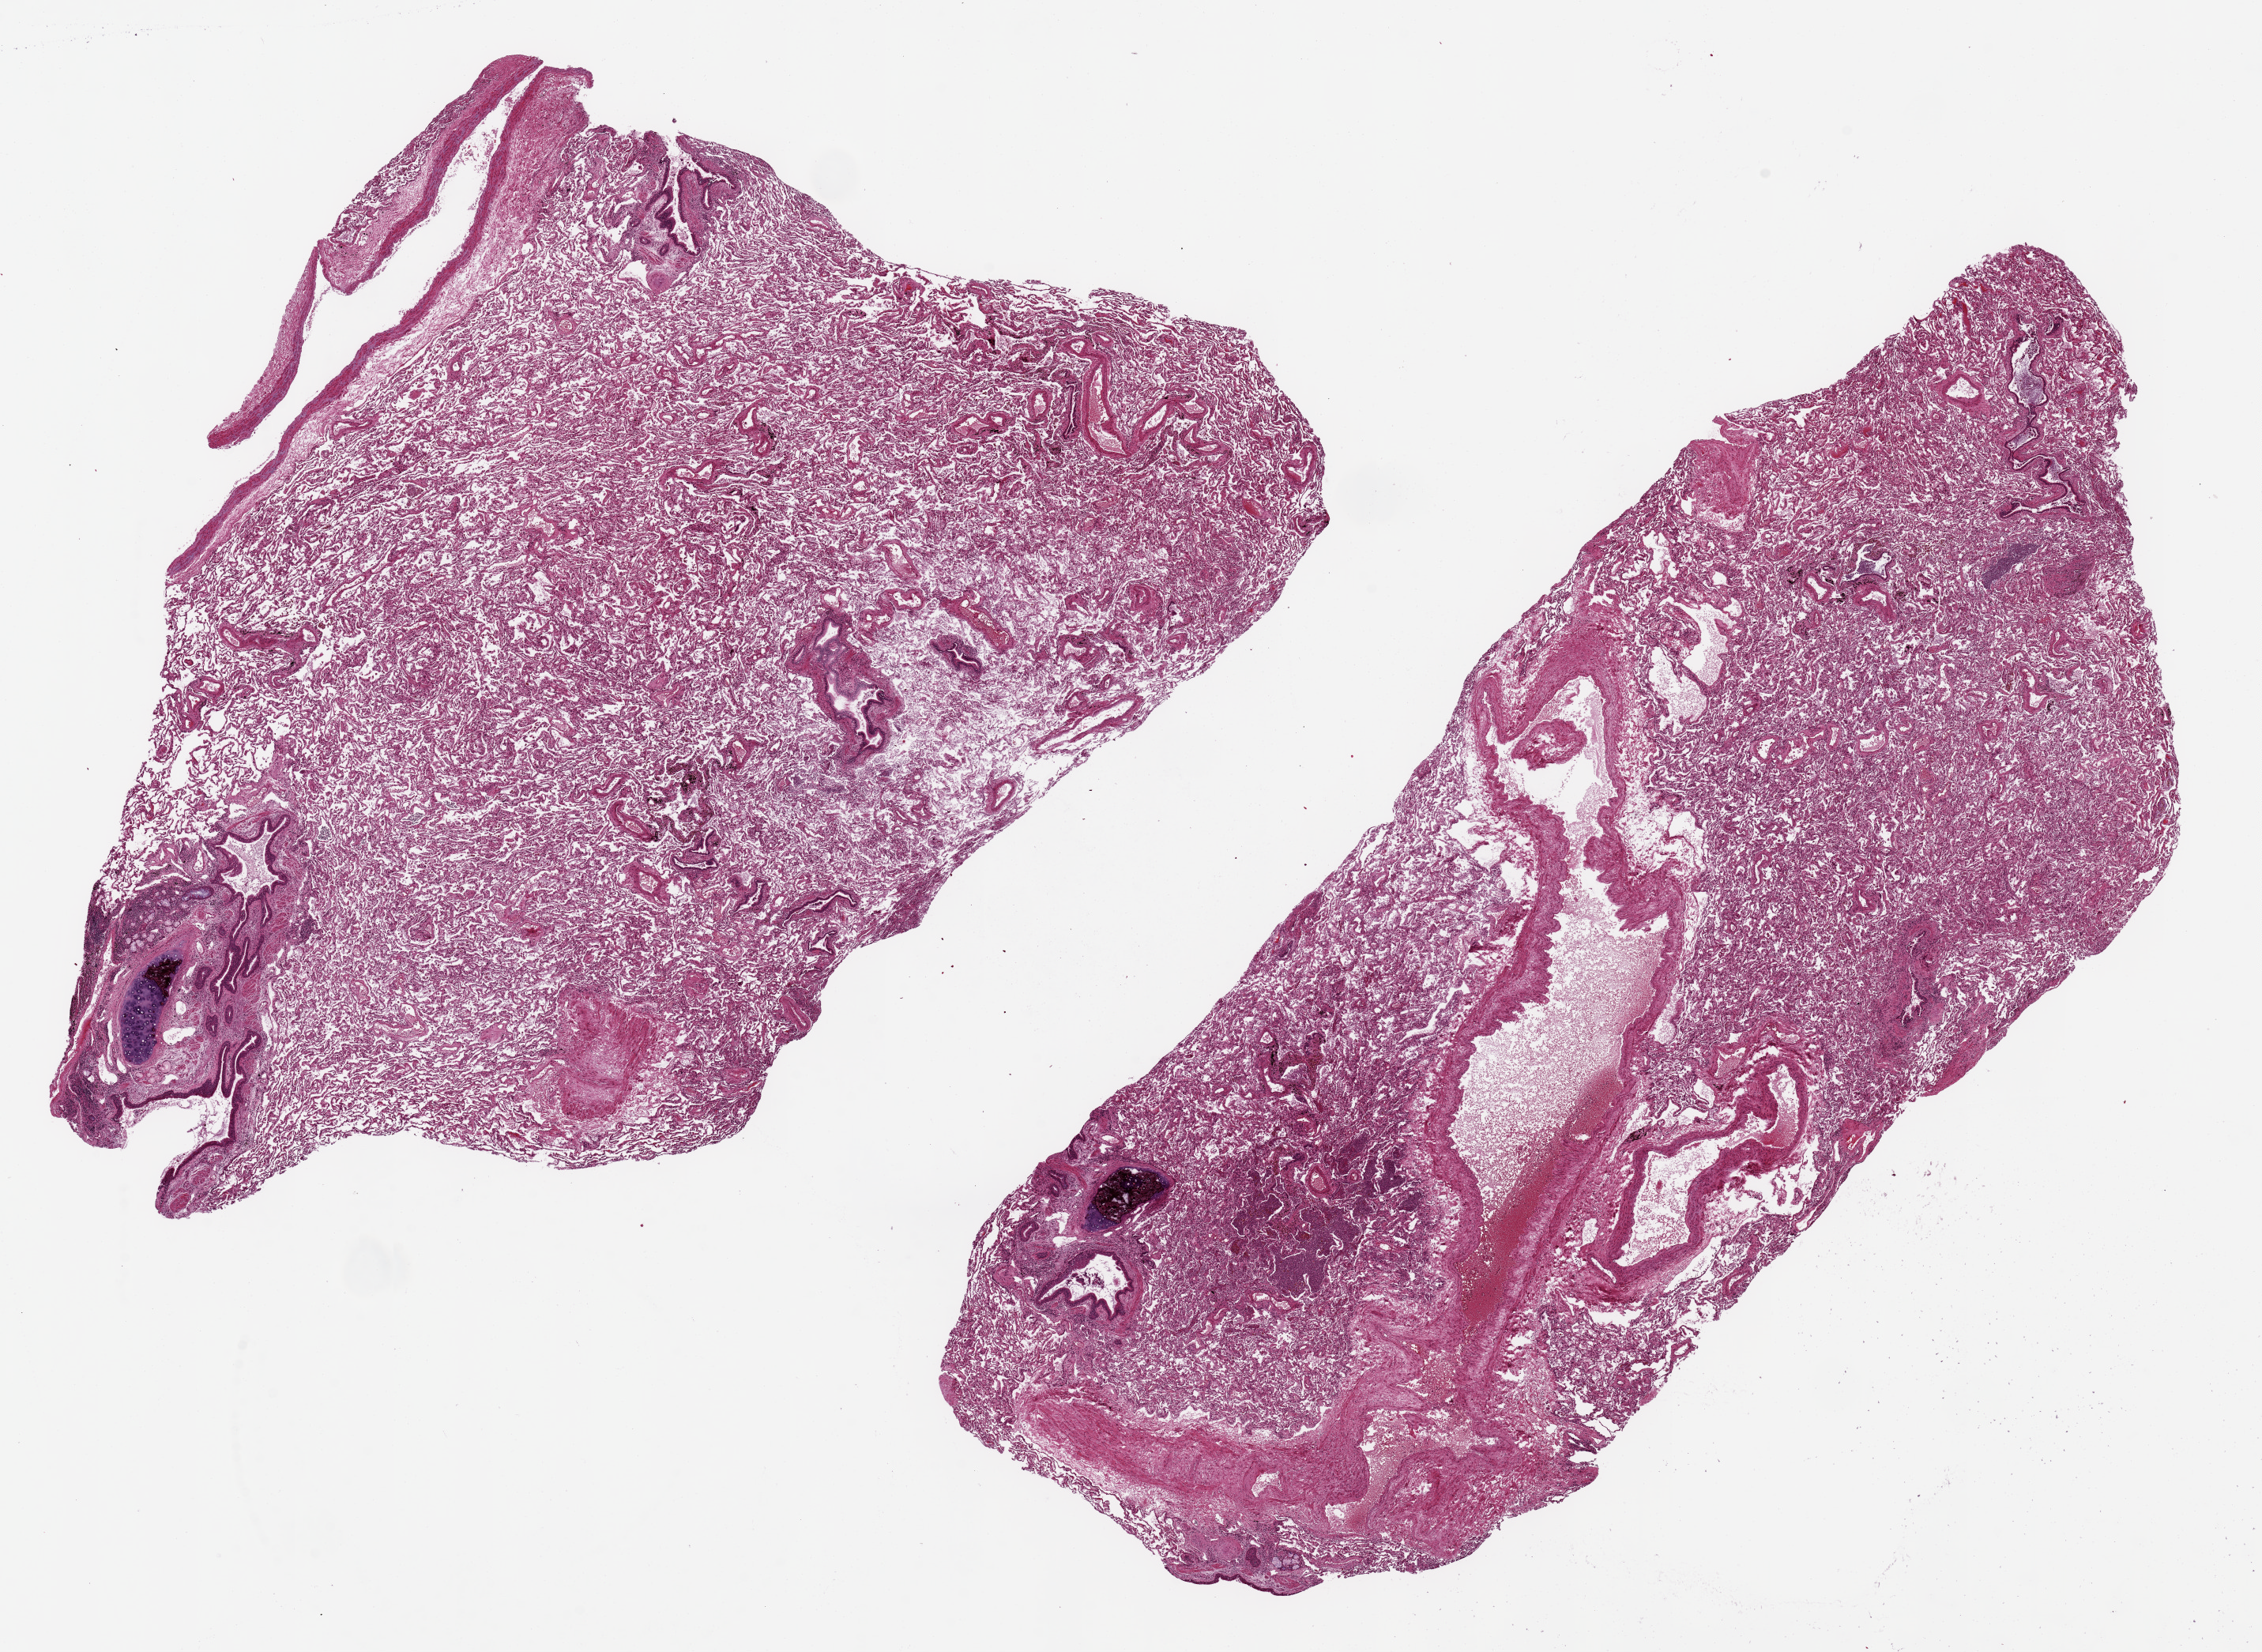
Digitized hematoxylin and eosin (H&E)-stained section — a low-resolution overview of the entire scanned area, about 22.6 x 16.5 mm, PAXgene-fixed, paraffin-embedded tissue, sampled site (target tissue): lung, donor tissue sample. Donor sex: male.
• pathologist's review note for this sample: 2 ~13x7mm aliquots. Diffuse mild acute pneumonia/mild congestion